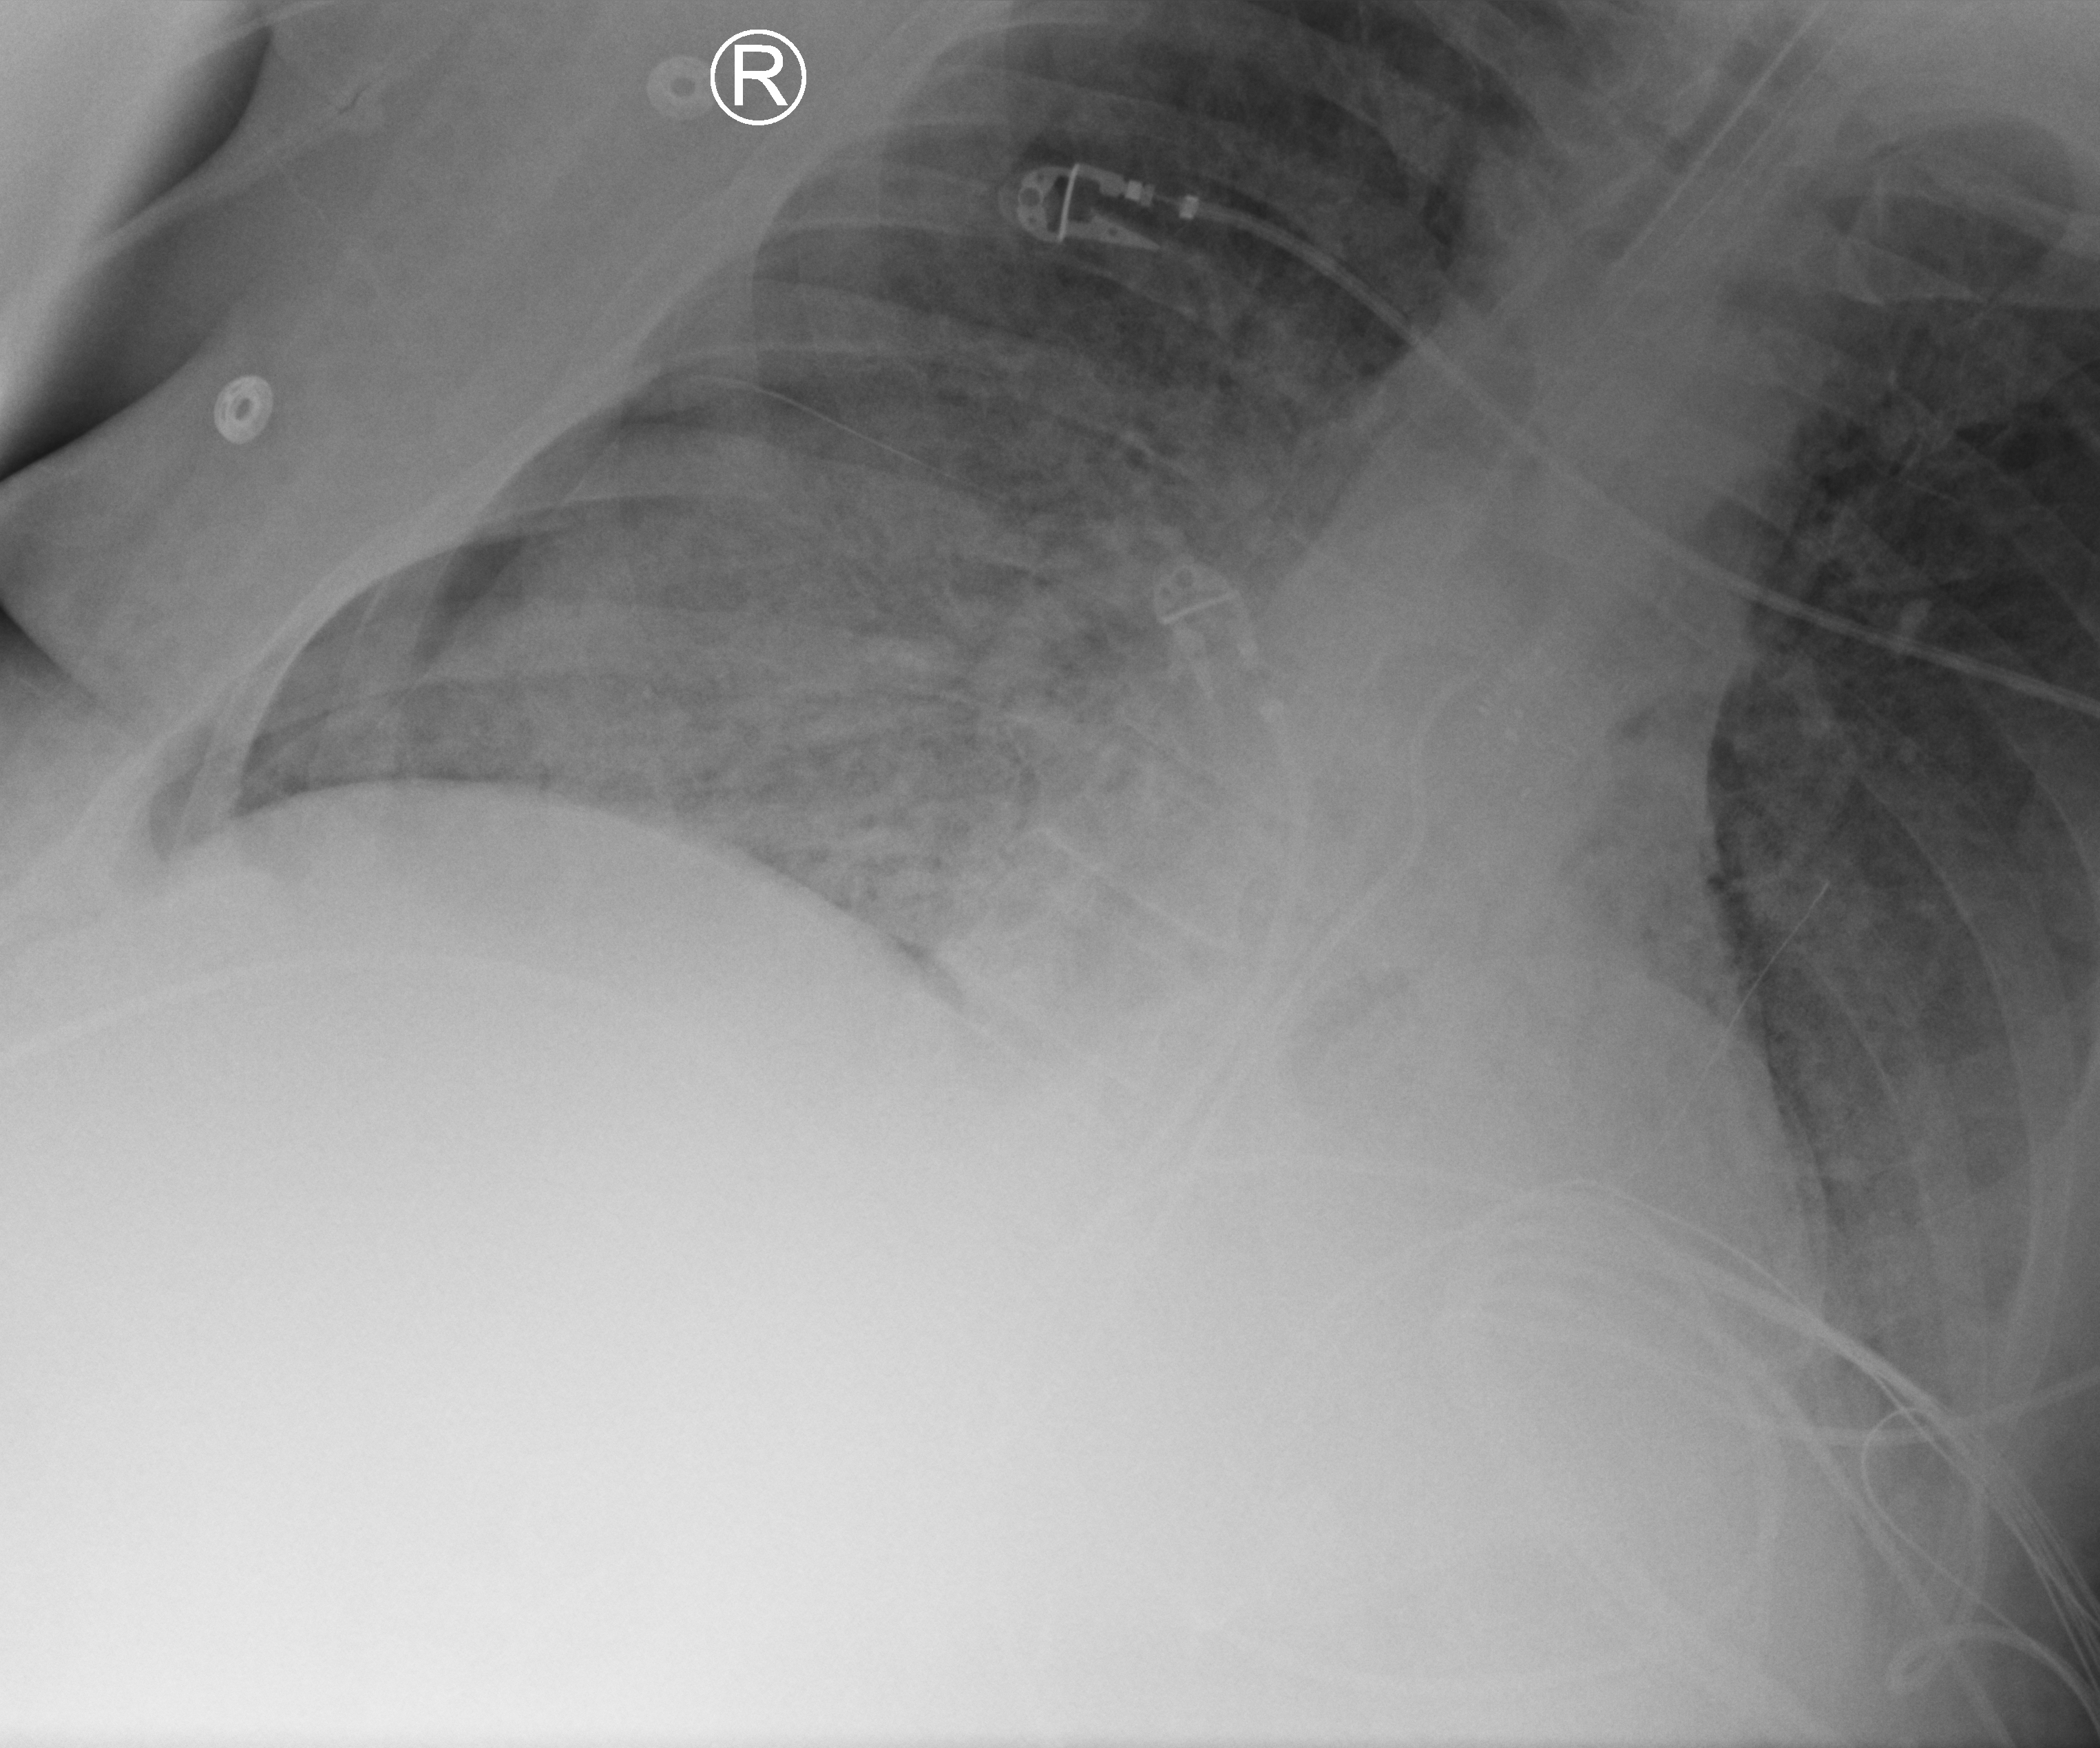
Bedside chest radiograph (computed radiography). Adult patient hospitalised with COVID-19, age 18–59 years.
Hospital-stay facts (about this admission, not read from this image; timing relative to this image not recorded): admitted to intensive care during this hospital stay: yes; mechanically ventilated during this hospital stay: yes; diabetes (admission record): yes.